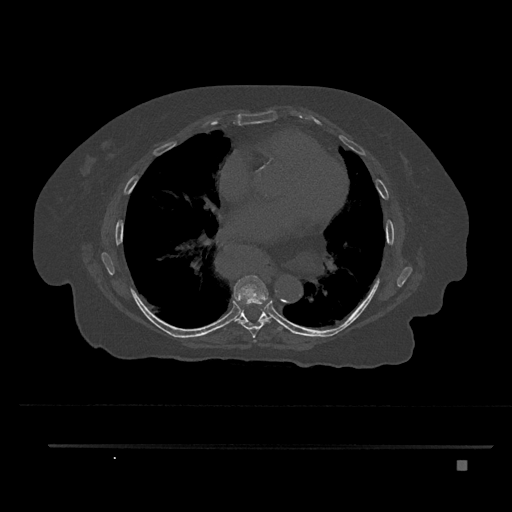
CT including the spine, one axial slice. Slice 466 of 797 in the series (ordered by position). Reconstruction kernel Br40s/3. Bone window (W 1800 / L 400 HU). 512 × 512 image matrix, field of view 437 × 437 mm. Female patient, age 76 years. Case-level facts recorded for this patient, not image findings: primary cancer: lung; vertebrae with lytic lesions (as recorded): T11, L3.
Outlined on this slice (semi-automatic segmentation, software-assisted and operator-edited):
- T6 vertebra: bounding box <253,340,256,343> (left, top, right, bottom; pixels)
- T7 vertebra: <234,275,272,338>
- T8 vertebra: <234,306,285,330>